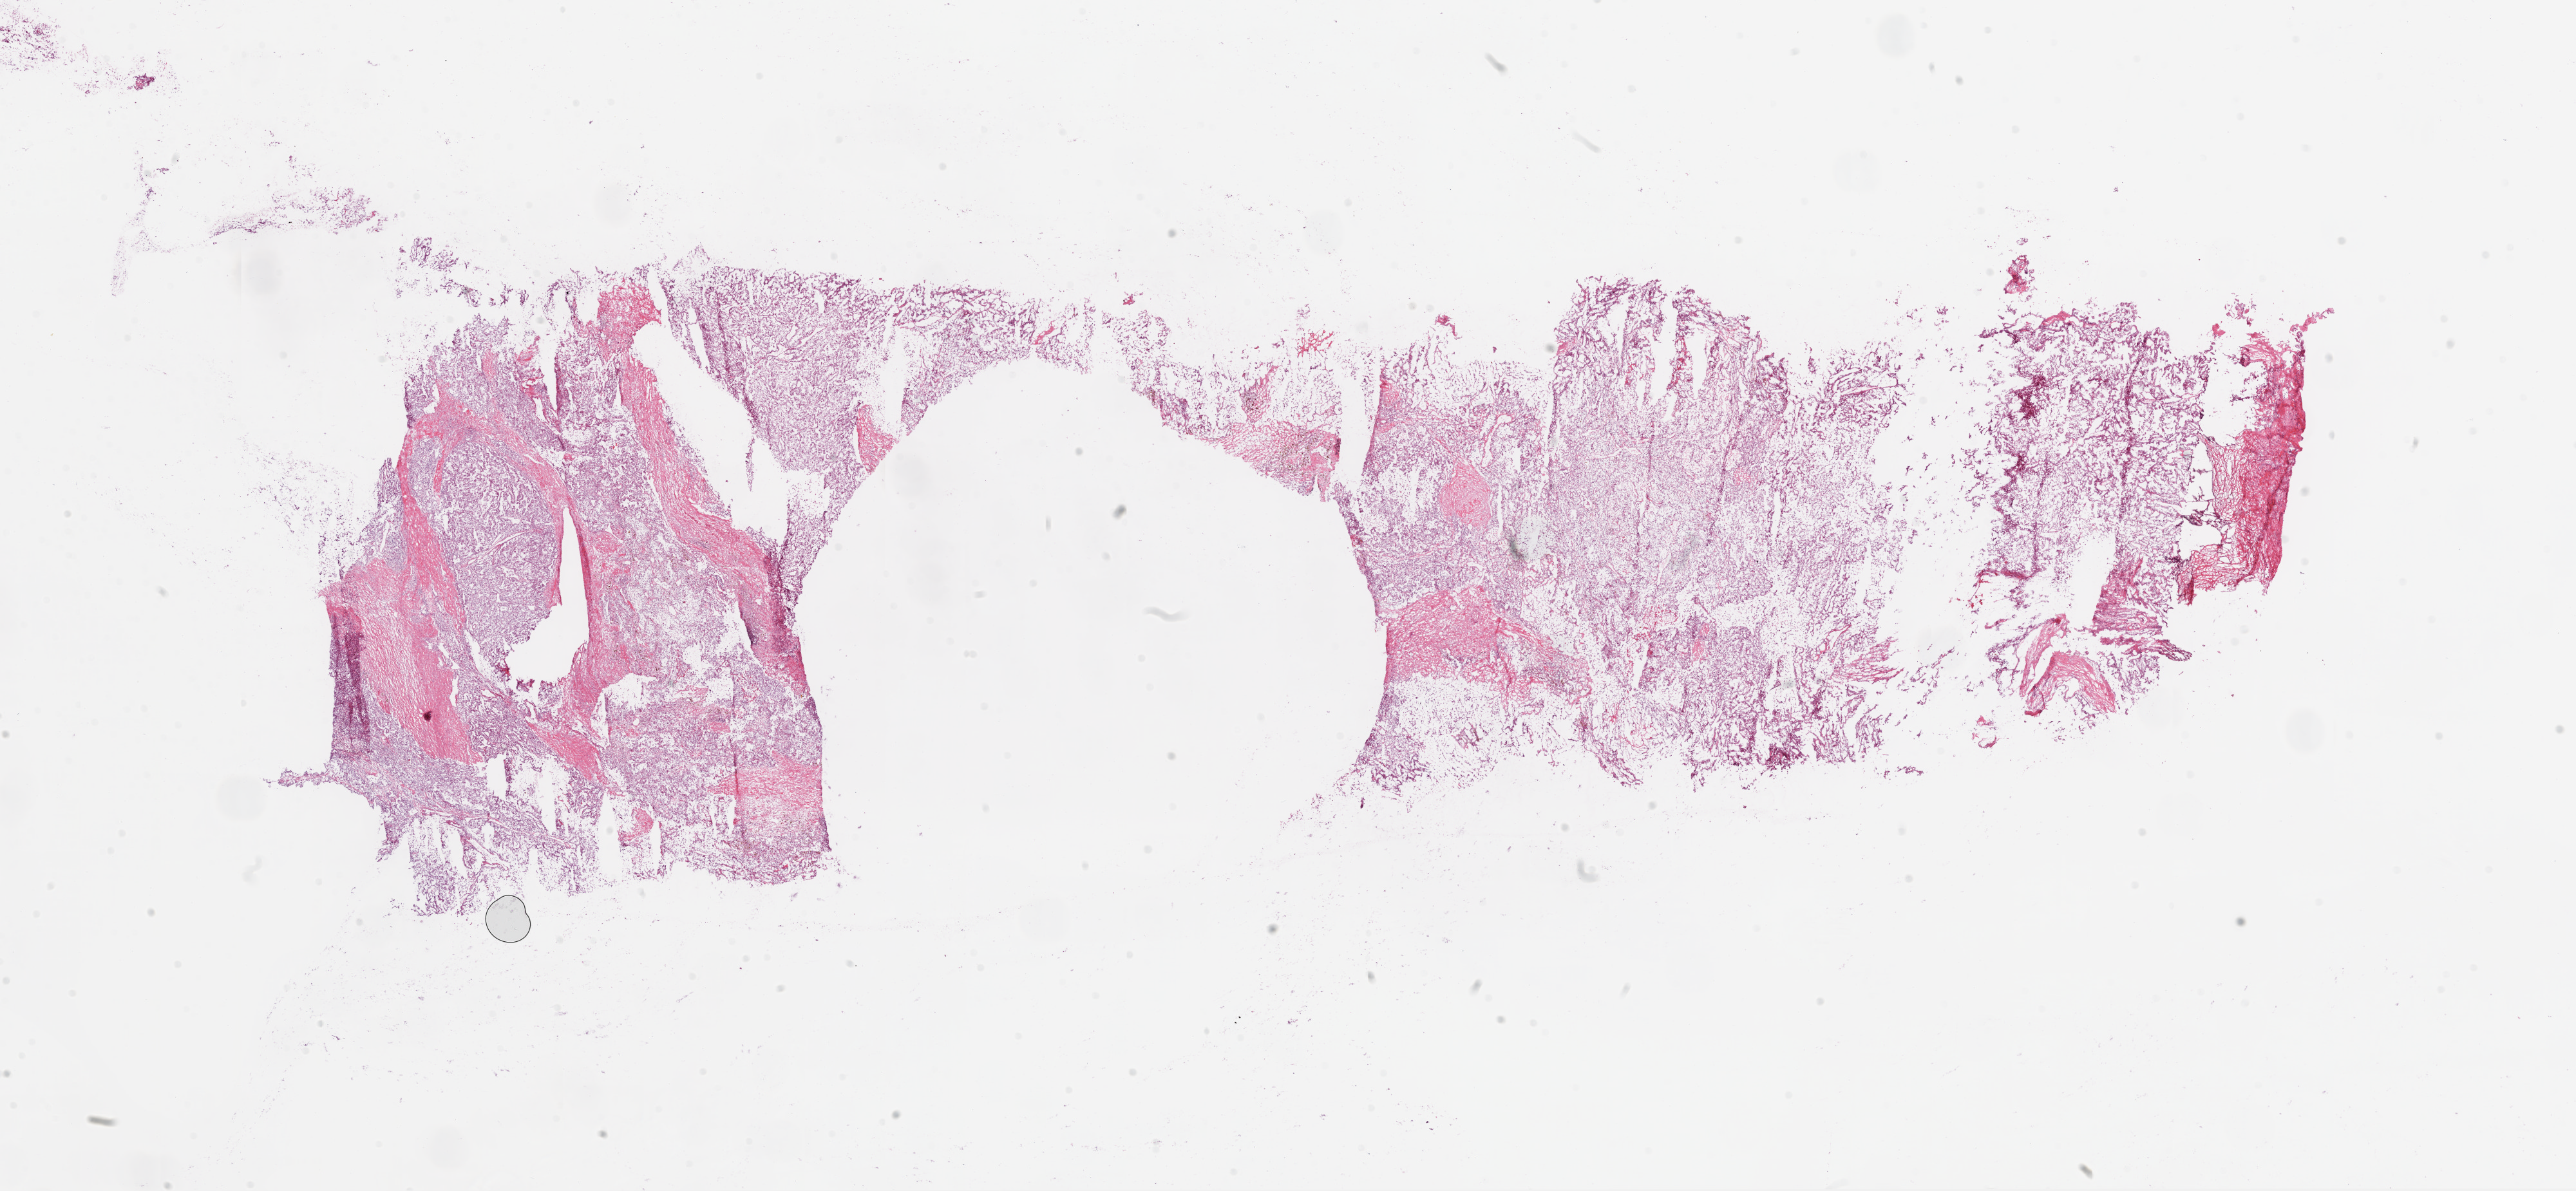
Digitized H&E tissue section (whole slide) — a low-resolution overview of the entire scanned area, about 32.1 x 14.8 mm (slide scanned at 20x); frozen section; kidney, primary tumour sample. Patient: male, age at initial diagnosis 51 years. Histologic grade: G3 (poorly differentiated). Composition of this section per pathologist review: tumour cells 80%, tumour nuclei 80%, normal cells 0%, stromal cells 20%, necrosis 0%.
AJCC pathologic stage: III. Lymph nodes positive (case pathology): 0 of 4 examined. Diagnosis: Clear cell adenocarcinoma, NOS.